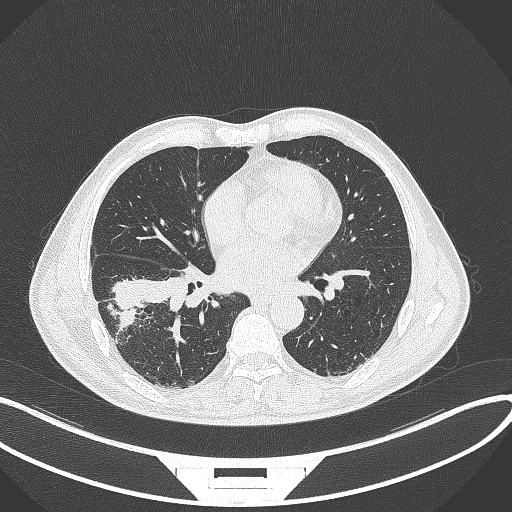
Chest CT, one axial slice; position 164 of 364 along the scan axis; reconstruction kernel B70f; 120 kVp; lung window (W 1500 / L -600 HU); 512 × 512 image matrix, field of view 400 × 400 mm. Patient: male, 58 years. From the clinical record (not read from this slice): clinical TNM (as recorded): T3 N0 M0; histopathological grade: G2.
Outlined on this slice (rectangle marked by the reading radiologist):
- lung tumour (recorded histology: squamous cell carcinoma): box from (x=111, y=275) to (x=172, y=325) px